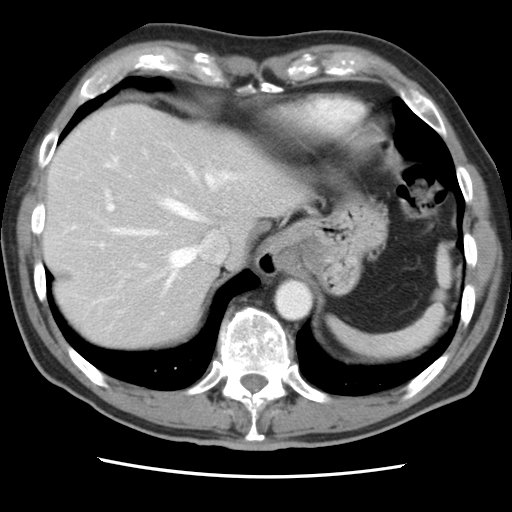
Contrast-enhanced abdominal CT, one axial slice; slice 68 of 83 in the series (ordered by position); 120 kVp; soft-tissue window (W 400 / L 40 HU); 5 mm slice thickness; 512 × 512 image matrix, field of view 321 × 321 mm. Male patient, age 69 years. Case-level facts recorded for this patient, not image findings: diagnosis: colorectal cancer liver metastases, imaged before liver resection; multiple liver metastases: yes; largest metastasis: 3.5 cm.
Structures marked on this image (expert manual segmentation):
- hepatic veins: bounding box [x1, y1, x2, y2] px = [74, 128, 235, 286]
- liver: [44, 105, 296, 350]
- planned liver remnant (the part of the liver to remain after resection): [44, 147, 217, 350]
- portal vein (with intrahepatic branches): [99, 189, 178, 267]